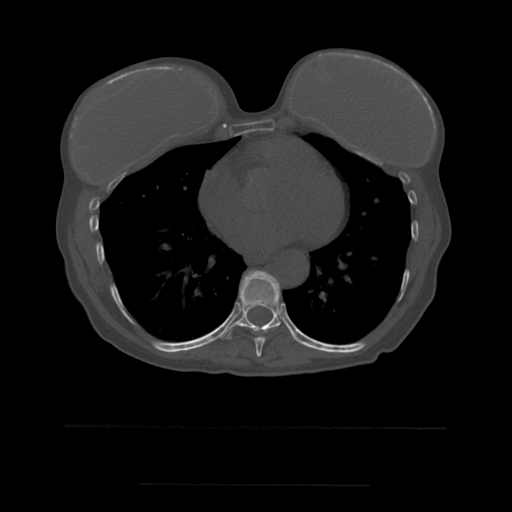
CT including the spine, one axial slice. Position 329 of 544 along the scan axis. Bone window (W 1800 / L 400 HU). 1.25 mm slice thickness. 512 × 512 image matrix, field of view 350 × 350 mm. Patient age 58 years. From the clinical record (not read from this slice): primary cancer: lung.
Structures marked on this image (semi-automatic segmentation, software-assisted and operator-edited):
- T8 vertebra: bounding box <246,274,279,357> (left, top, right, bottom; pixels)
- T9 vertebra: <217,270,281,340>